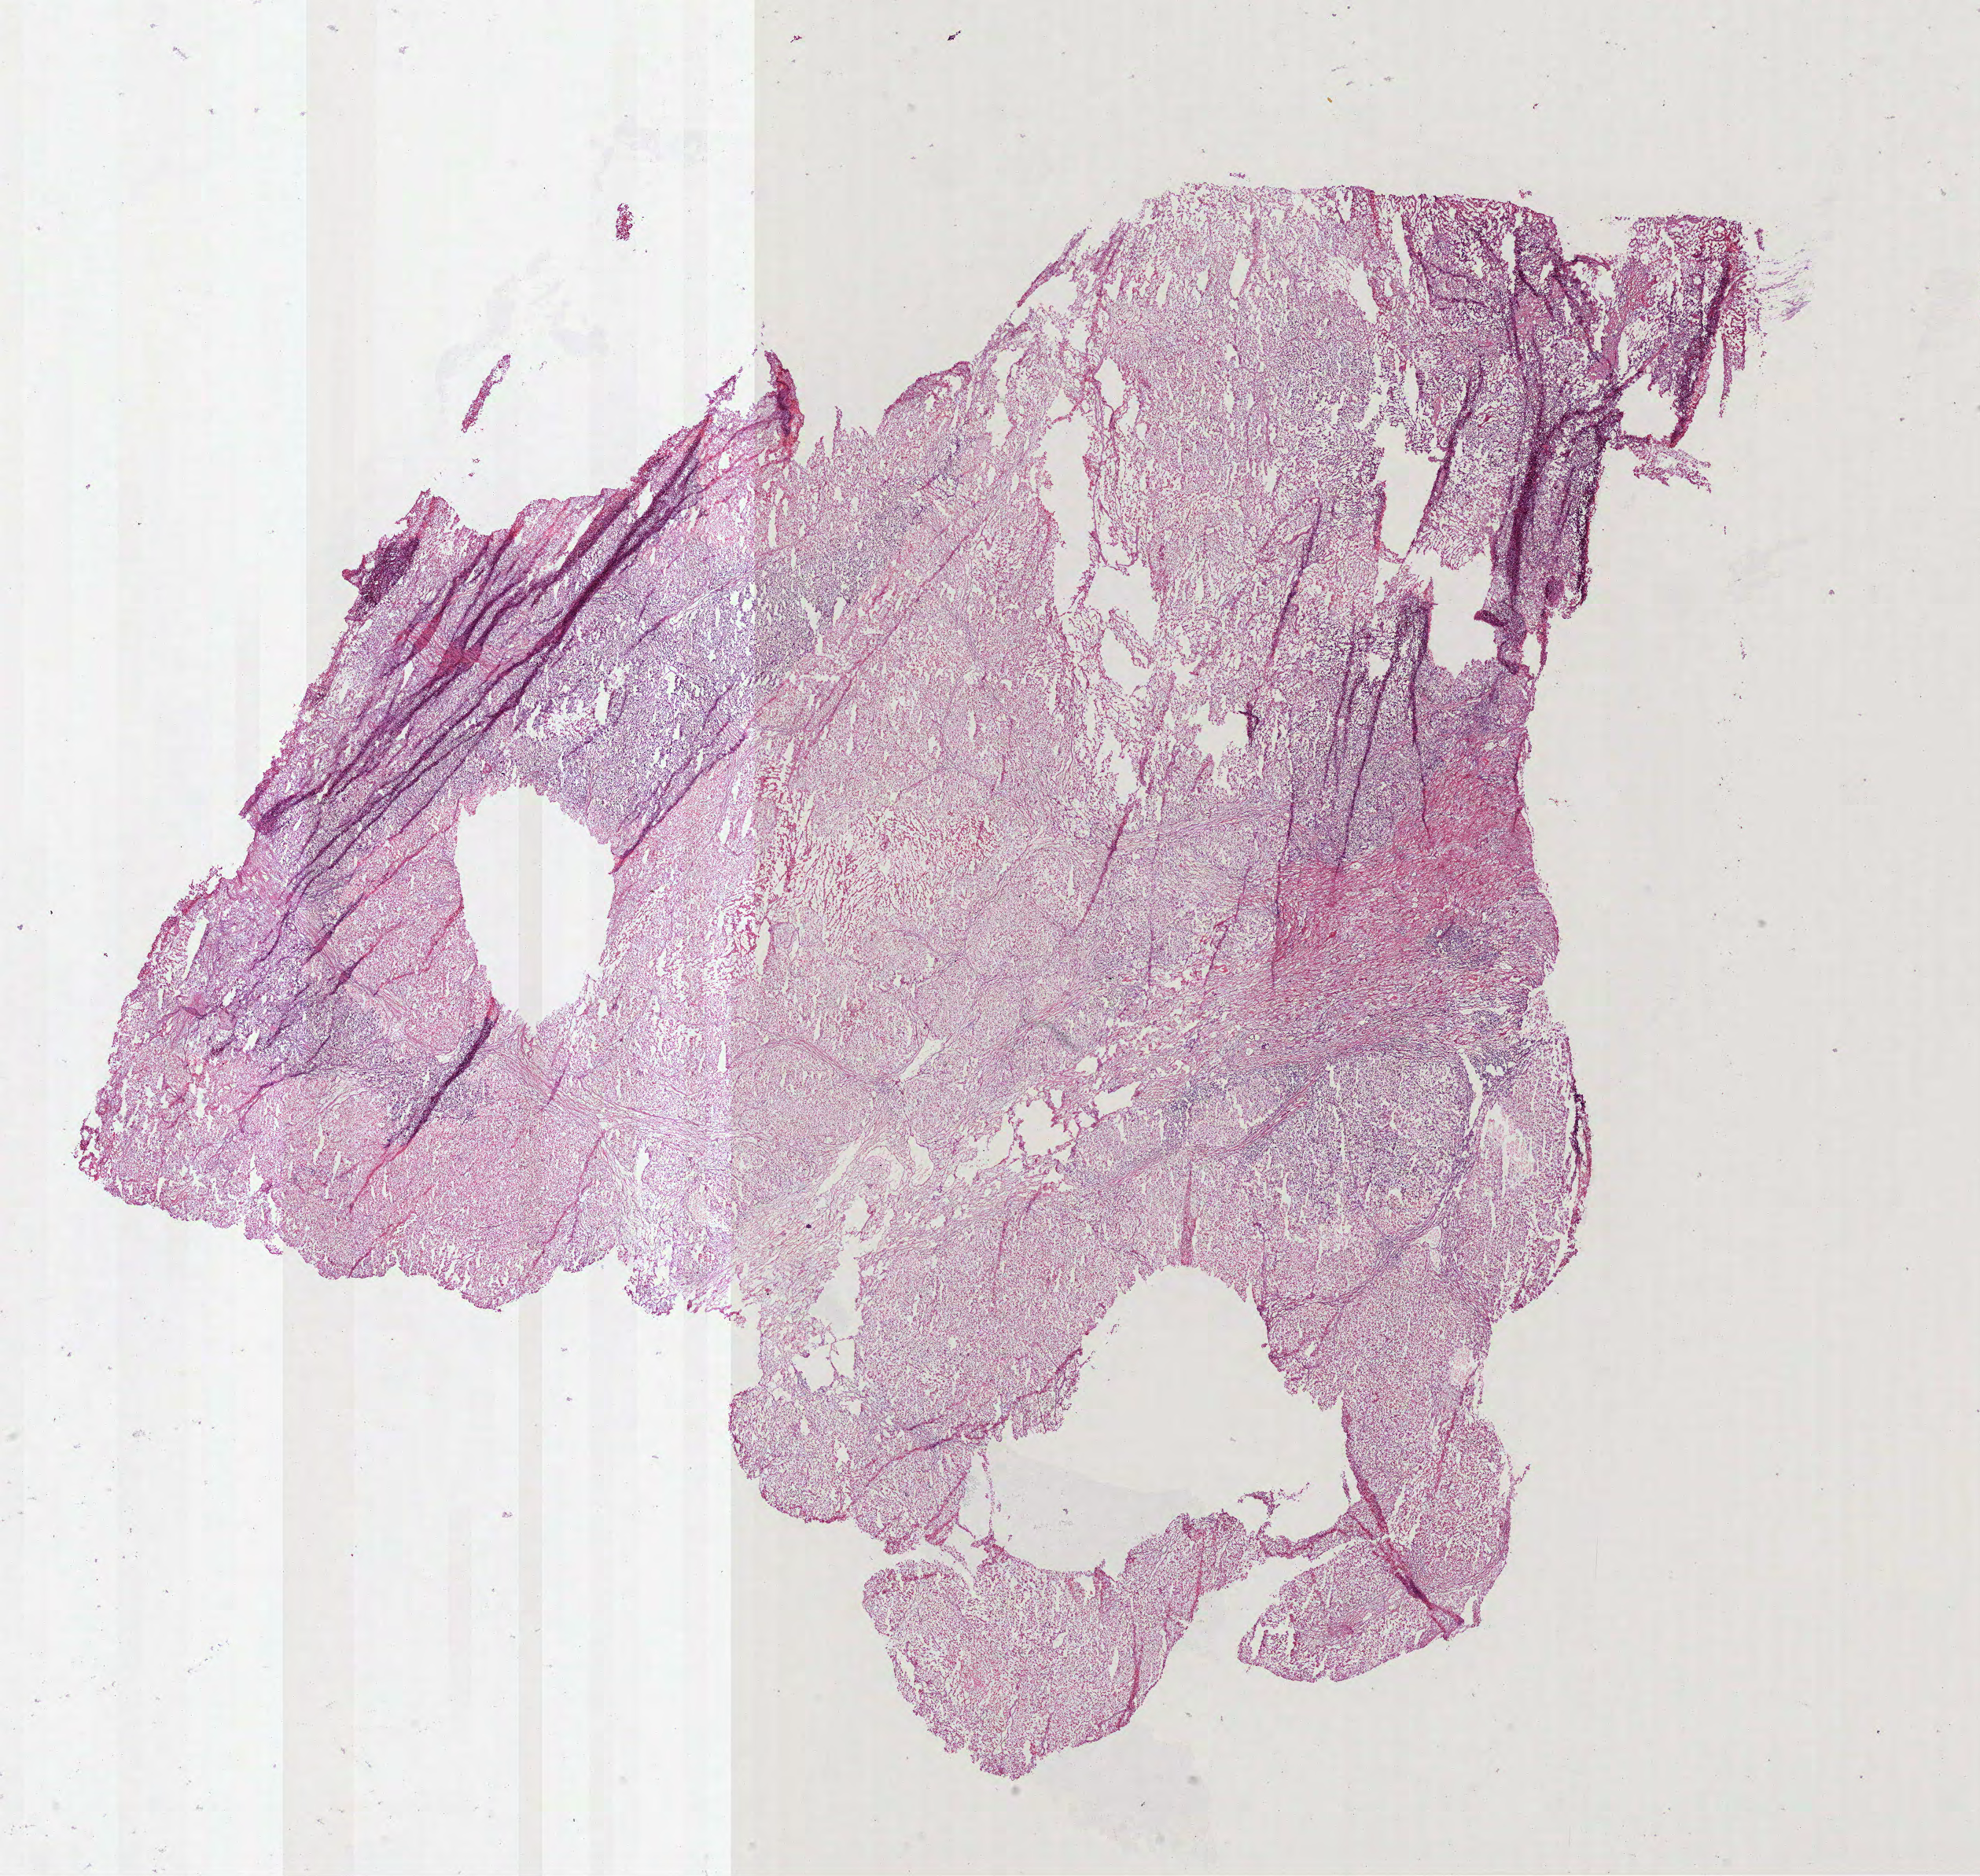
Digitized Hematoxylin and eosin (H&E) stained tissue section (whole slide), whole scanned area (about 20.3 x 19.2 mm) shown as a low-resolution overview; frozen section from the bottom of the tissue portion; sample: primary tumour, kidney. Patient: male, age at initial diagnosis 71 years. Pathologist review of this section (percent, as recorded): tumour cells 85%, tumour nuclei 85%, normal cells 0%, stromal cells 10%, necrosis 5%. Infiltration values recorded for this section: lymphocyte infiltration 6%, monocyte infiltration 0%, neutrophil infiltration 0%.
* laterality: left
* AJCC pathologic stage: II (6th edition)
* lymph nodes positive (case pathology): 0 of 1 examined
* diagnosis: Renal cell carcinoma, chromophobe type